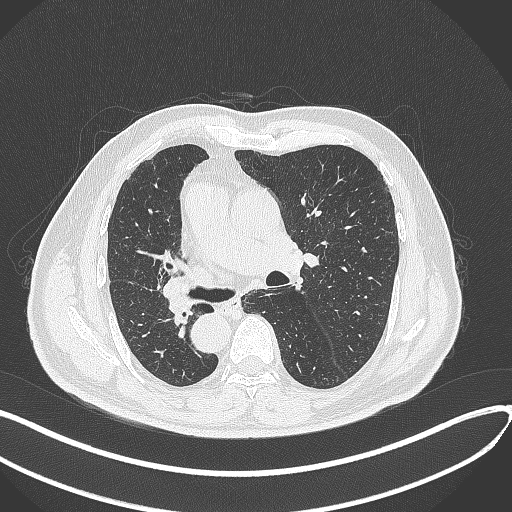
Chest CT, one axial slice. Slice 163 of 300 in the series (ordered by position). 120 kVp. Lung window (W 1500 / L -600 HU). 1 mm slice thickness. 512 × 512 image matrix, field of view 400 × 400 mm. Male patient, age 67 years. Case-level facts recorded for this patient, not image findings: clinical TNM (as recorded): T2a N0 M0.
Outlined on this slice (rectangle marked by the reading radiologist):
- lung tumour (recorded histology: squamous cell carcinoma): bounding box (x1, y1, x2, y2) in pixels: (158, 275, 198, 321)